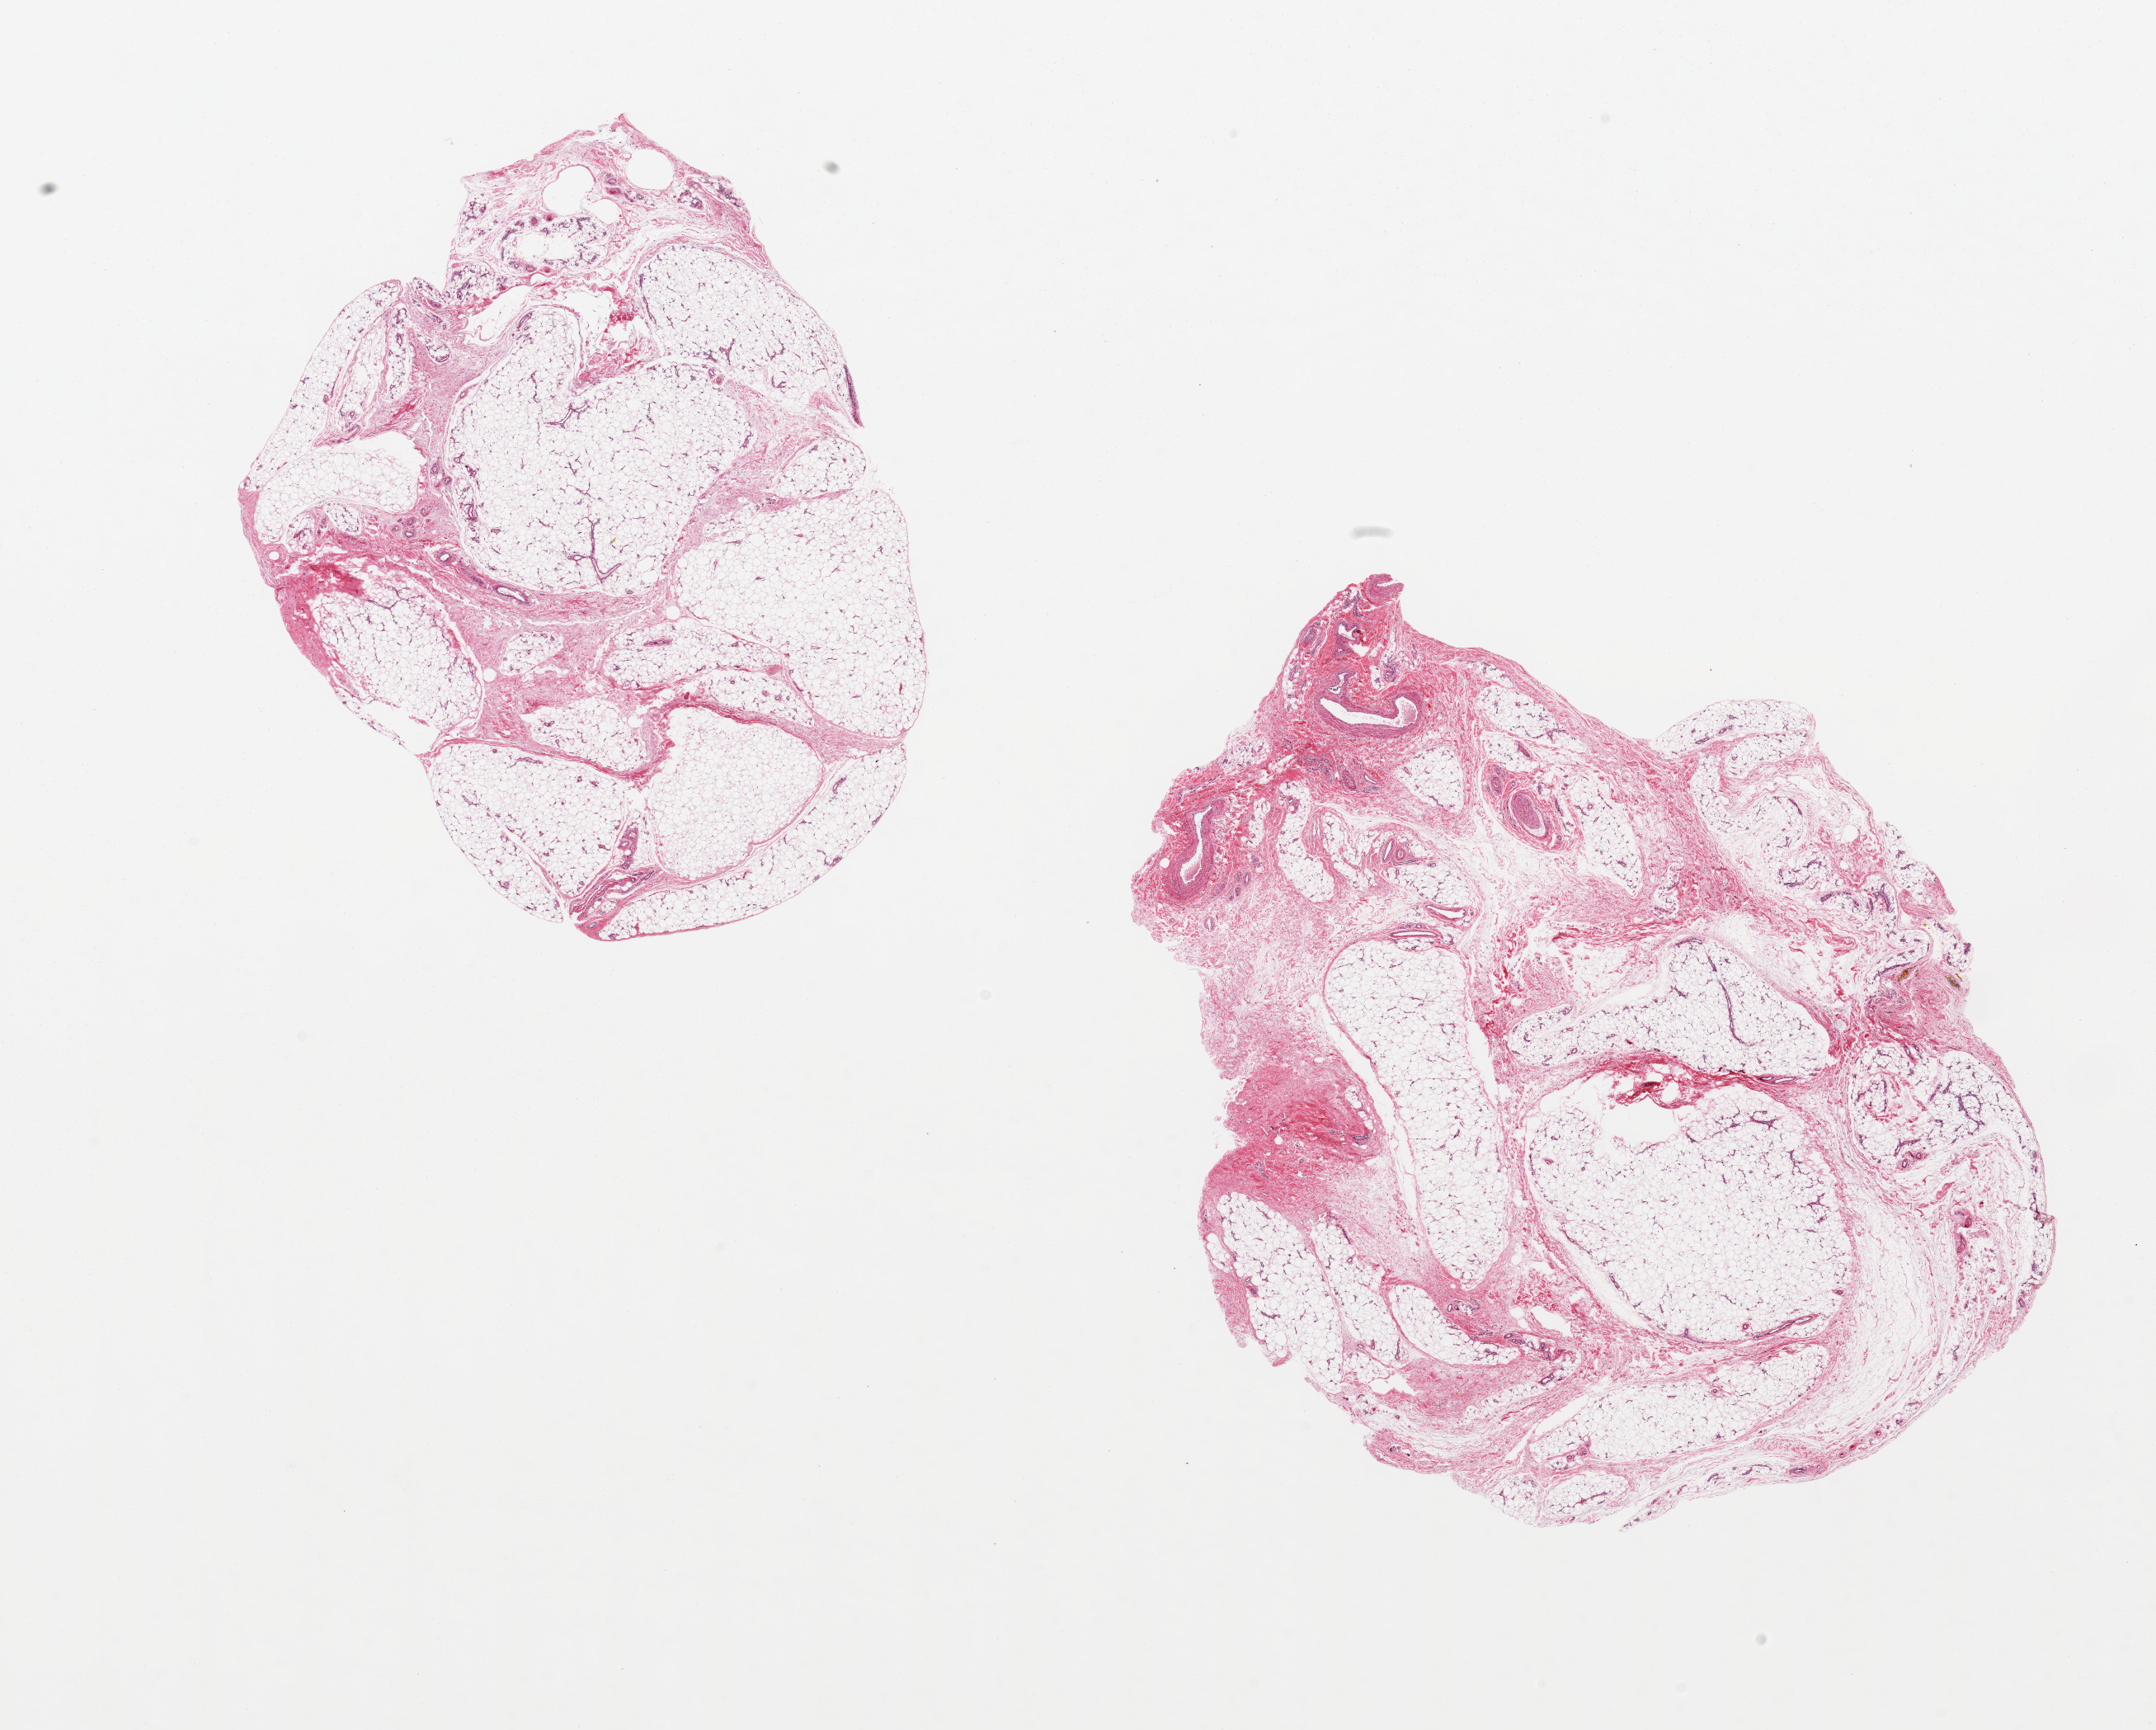
H&E whole-slide image, low-resolution overview of the scanned area, about 20.7 x 16.6 mm; PAXgene-fixed, paraffin-embedded tissue; sampled site (target tissue): adipose tissue; tissue donor sample. Donor: male.
Review note (as recorded): 2 pieces, 9x8 &&7x6 mm; larger piece has adjacent veins on one side [~10%].